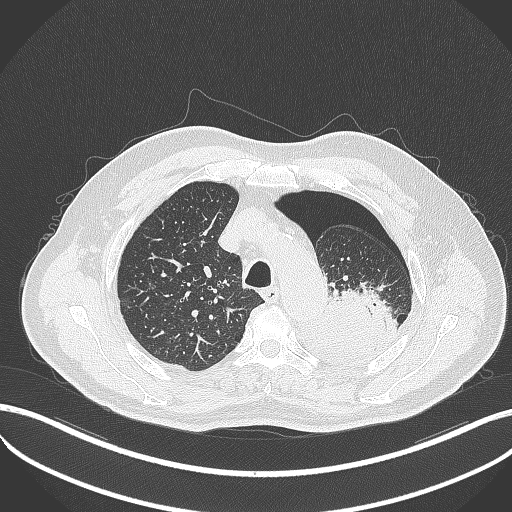
Chest CT, one axial slice. Slice 392 of 464 in the series (ordered by position). Reconstruction kernel B70f. 120 kVp. Lung window (W 1500 / L -600 HU). 1 mm slice thickness. 512 × 512 image matrix. Patient: male, 76 years. Case-level facts recorded for this patient, not image findings: clinical TNM (as recorded): T3 N0 M1b.
Structures marked on this image (bounding box drawn by a radiologist):
- lung tumour (recorded histology: adenocarcinoma): box from (x=315, y=285) to (x=398, y=367) px